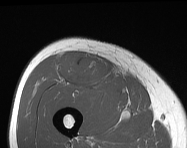
MRI of an extremity soft-tissue mass, one axial slice. Position 67 of 114 along the scan axis. MR volume resampled by the dataset authors to the PET/CT grid (not the native acquisition matrix). 3.27 mm slice thickness. 187 × 148 image matrix. Male patient. From the clinical record (not read from this slice): histological type: pleiomorphic leiomyosarcoma; grade: intermediate; site of the primary tumour: right thigh.
Annotated regions visible in this slice (expert contour drawn on MRI and transferred to this co-registered scan by the dataset authors):
- gross tumour volume including surrounding oedema: bounding box [x1, y1, x2, y2] px = [57, 52, 110, 87]
- gross tumour volume (mass): [73, 59, 105, 83]